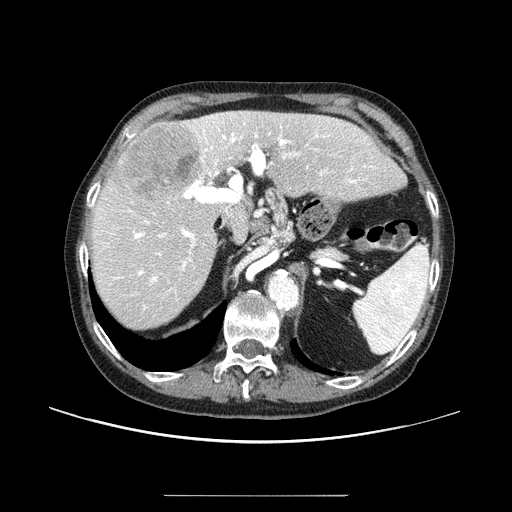
Contrast-enhanced abdominal CT (liver protocol), one axial slice; slice 61 of 91 in the series (ordered by position); reconstruction kernel STANDARD; one of 2 acquisitions stored at this slice position; soft-tissue window (W 400 / L 40 HU); 2.5 mm slice thickness; 512 × 512 image matrix. Case-level facts recorded for this patient, not image findings: diagnosis: hepatocellular carcinoma (patient treated with transarterial chemoembolisation; whether this scan precedes or follows treatment is not stated here); TNM stage (as recorded): Stage-I; Child-Pugh class: A; tumour nodularity: uninodular.
Annotated regions visible in this slice (semi-automatically segmented with operator editing):
- liver parenchyma outside the tumour (the mass and vessels are separate outlines, so this box may not span the whole liver): bounding box (x1, y1, x2, y2) in pixels: (90, 110, 376, 328)
- mass: (111, 123, 201, 200)
- liver vessels: (97, 113, 369, 309)